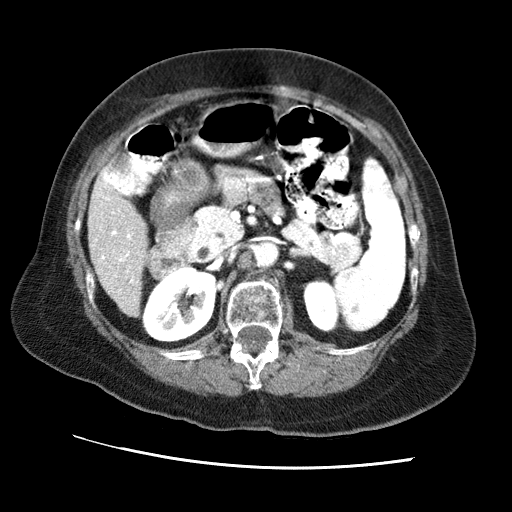
Contrast-enhanced abdominal CT (liver protocol), one axial slice; position 23 of 65 along the scan axis; reconstruction kernel STANDARD; 120 kVp; soft-tissue window (W 400 / L 40 HU); 2.5 mm slice thickness; 512 × 512 image matrix, field of view 340 × 340 mm. Case-level facts recorded for this patient, not image findings: diagnosis: hepatocellular carcinoma (patient treated with transarterial chemoembolisation; whether this scan precedes or follows treatment is not stated here); TNM stage (as recorded): Stage-II; Child-Pugh class: A; tumour differentiation: no biopsy; tumour nodularity: multinodular.
Annotated regions visible in this slice (semi-automatic segmentation, software-assisted and operator-edited):
- liver parenchyma outside the tumour (the mass and vessels are separate outlines, so this box may not span the whole liver): bounding box (x1, y1, x2, y2) in pixels: (88, 184, 146, 316)
- liver vessels: (95, 185, 134, 282)